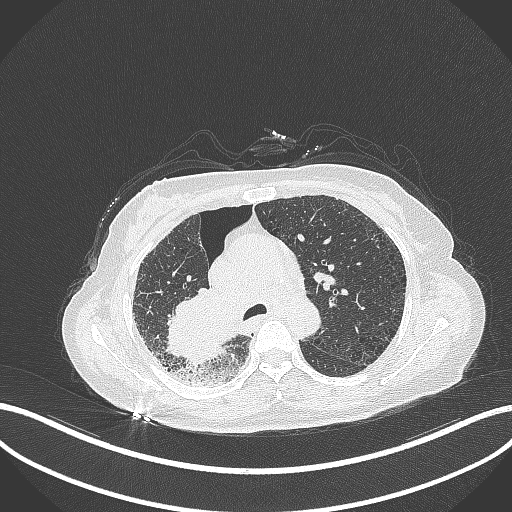
Chest CT, one axial slice; position 230 of 408 along the scan axis; reconstruction kernel B70f; 120 kVp; lung window (W 1500 / L -600 HU); 1 mm slice thickness; 512 × 512 image matrix, field of view 400 × 400 mm. Patient: female, 64 years. Case-level facts recorded for this patient, not image findings: clinical TNM (as recorded): T3 N3 M0.
Annotated regions visible in this slice (rectangle marked by the reading radiologist):
- lung tumour (recorded histology: squamous cell carcinoma): bounding box [x1, y1, x2, y2] px = [164, 286, 229, 372]